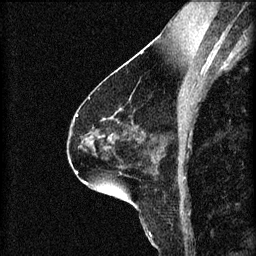
Breast MRI (dynamic contrast-enhanced), one sagittal slice. 3 images stored at this slice position (order not interpretable as contrast timing). 1.5 T. TE 4.2 ms, TR 8.2 ms. 2 mm slice thickness. 256 × 256 image matrix, field of view 180 × 180 mm. Female patient, age 60 years.
Annotated regions visible in this slice (semi-automatic segmentation, software-assisted and operator-edited):
- analysis volume of interest (the breast-tissue region the enhancement analysis was run in; not a lesion): bounding box [x1, y1, x2, y2] px = [89, 118, 127, 151]
- tumour enhancement mask (voxels above the 70 % enhancement threshold inside the analysis volume of interest): [103, 118, 105, 121]